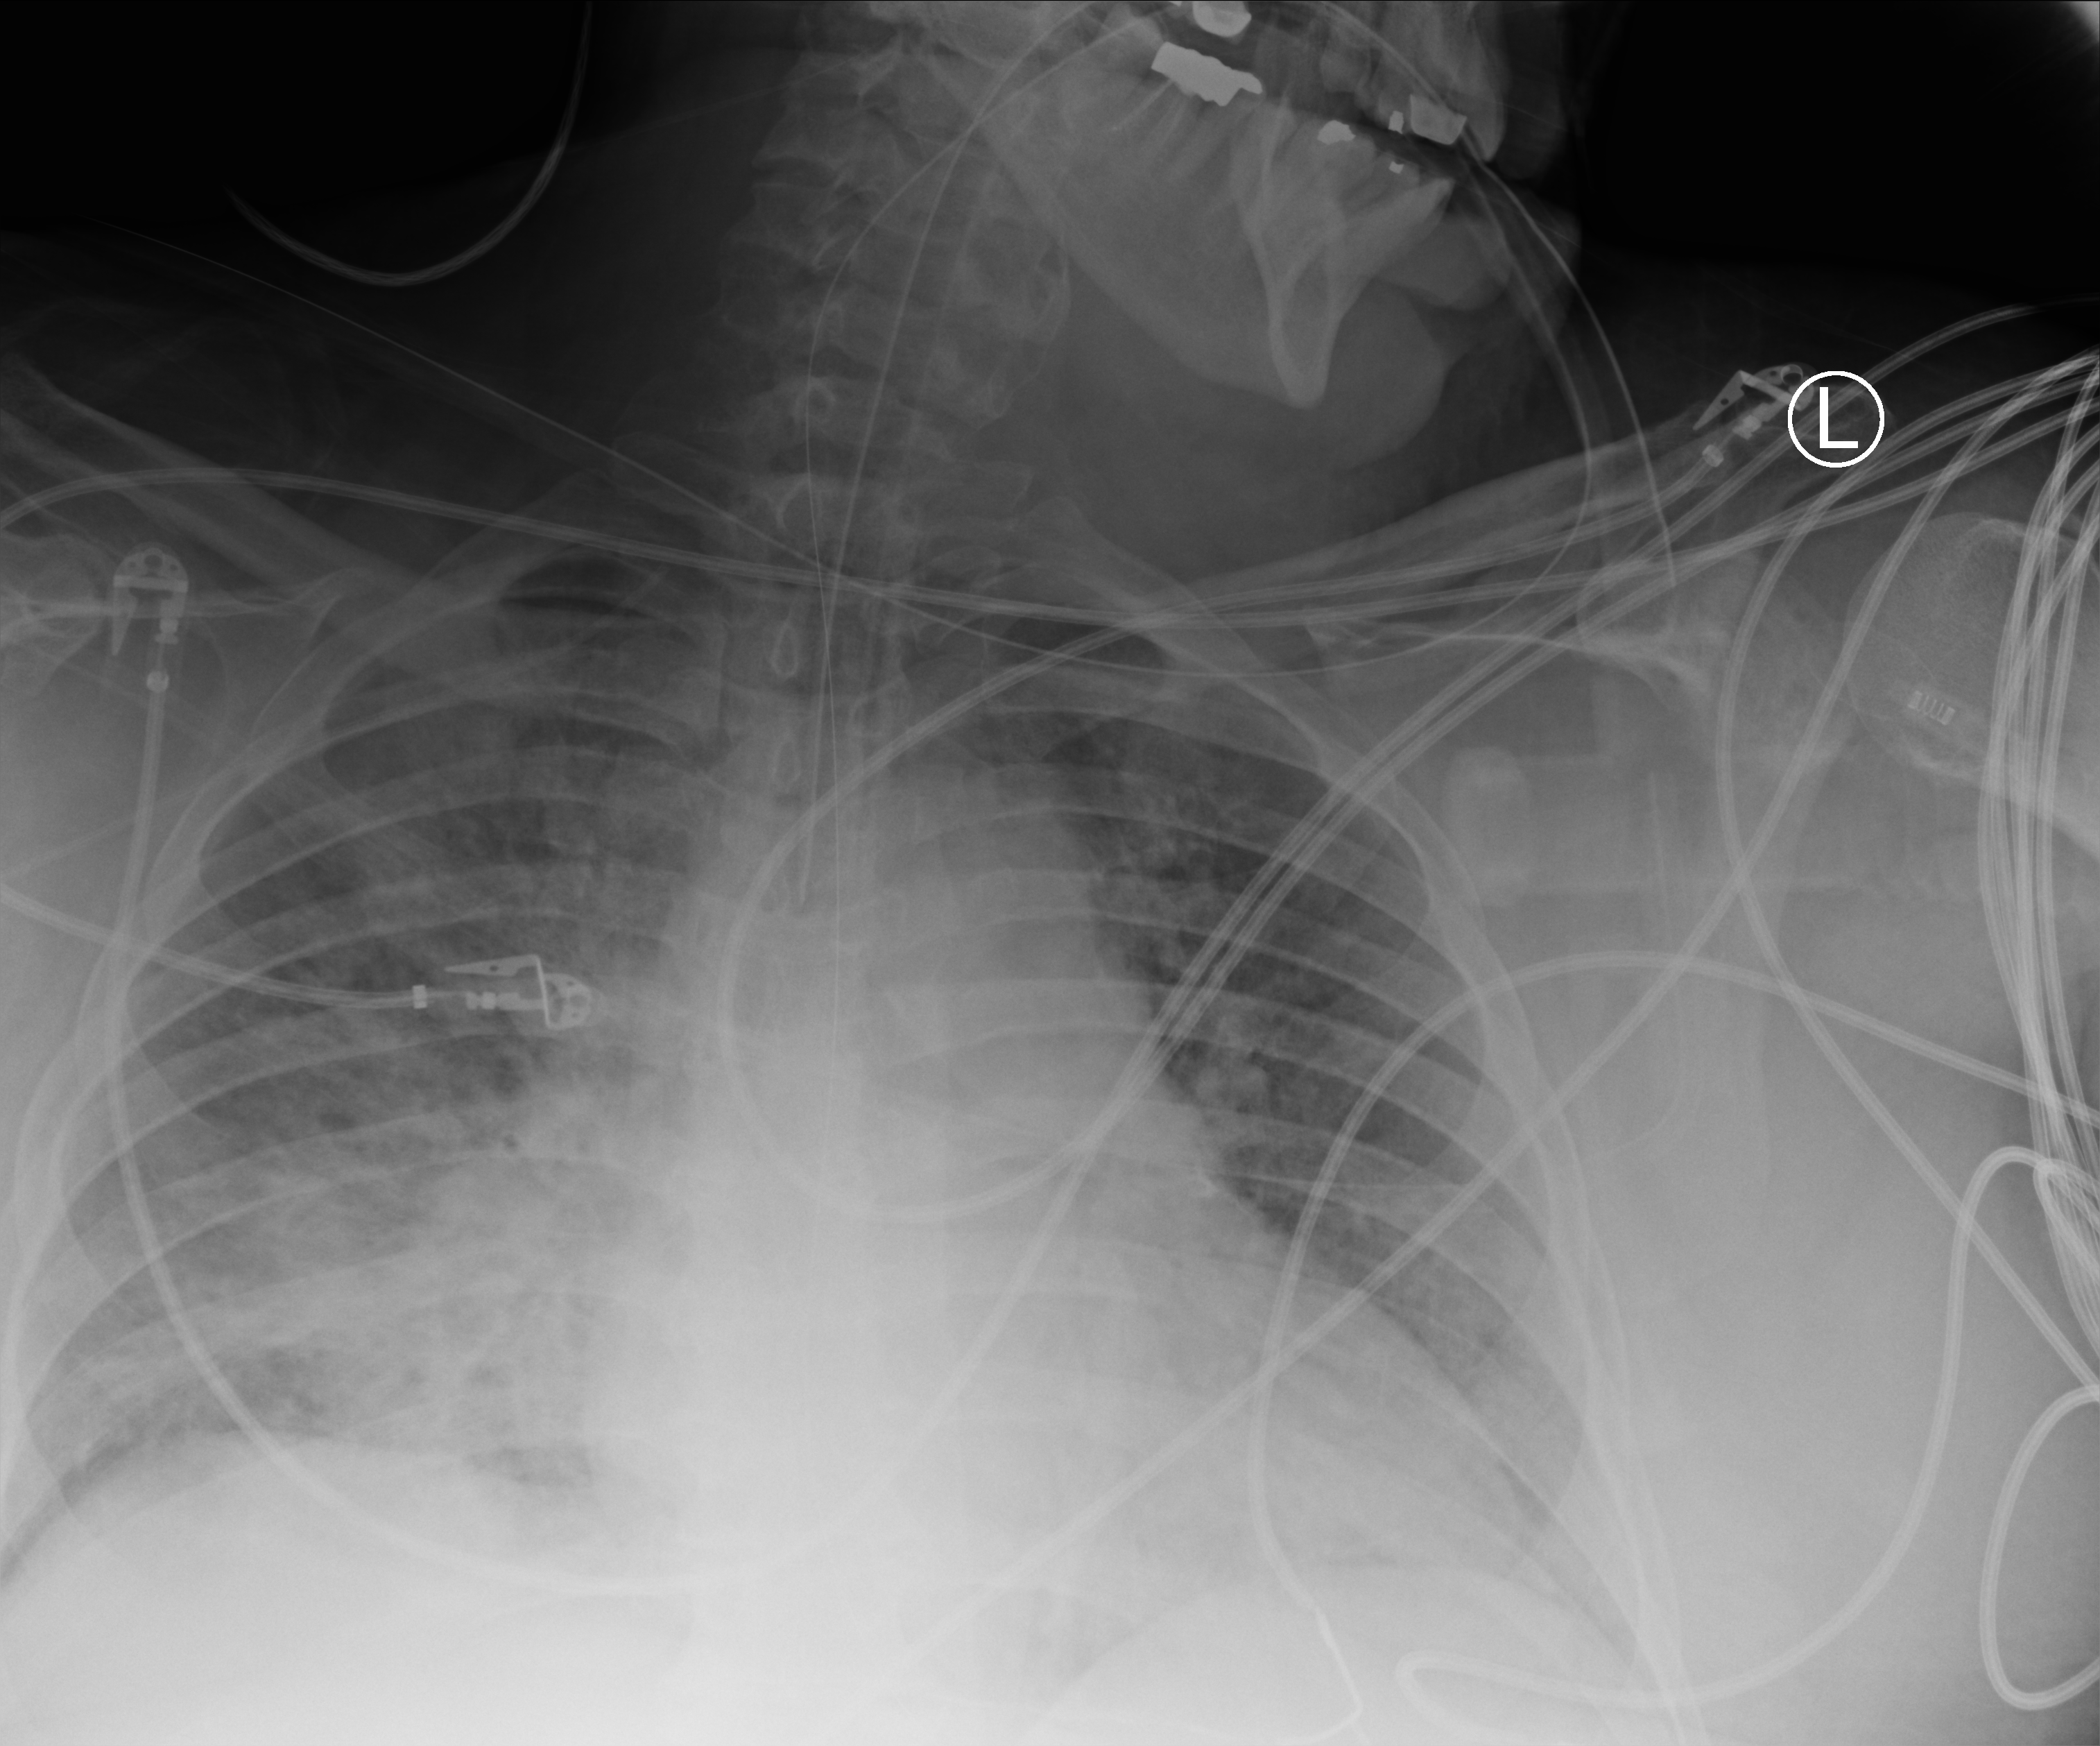
Portable chest radiograph, anteroposterior (AP) projection. Patient hospitalised with COVID-19; male, aged 18–59 years.
From the hospital-stay record, not from the radiograph (when in the stay this image was taken is not recorded):
- COPD (admission record): no
- other chronic lung disease (admission record): no